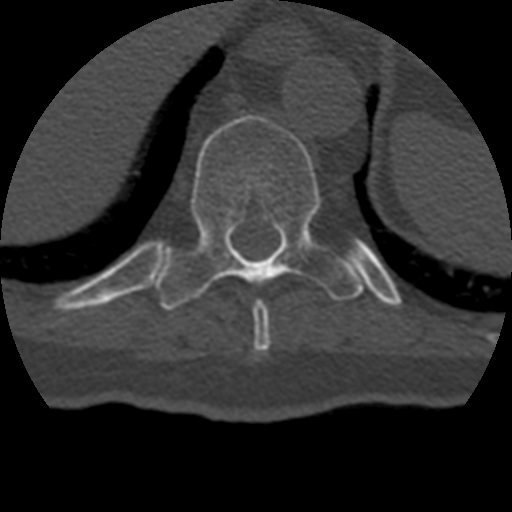
CT including the spine, one axial slice. Position 222 of 399 along the scan axis. Bone window (W 1800 / L 400 HU). 1.25 mm slice thickness. 512 × 512 image matrix, field of view 160 × 160 mm. Patient age 69 years. Case-level facts recorded for this patient, not image findings: primary cancer: prostate.
Annotated regions visible in this slice (semi-automatically segmented with operator editing):
- T10 vertebra: bounding box <156,115,363,310> (left, top, right, bottom; pixels)
- T9 vertebra: <253,300,271,355>